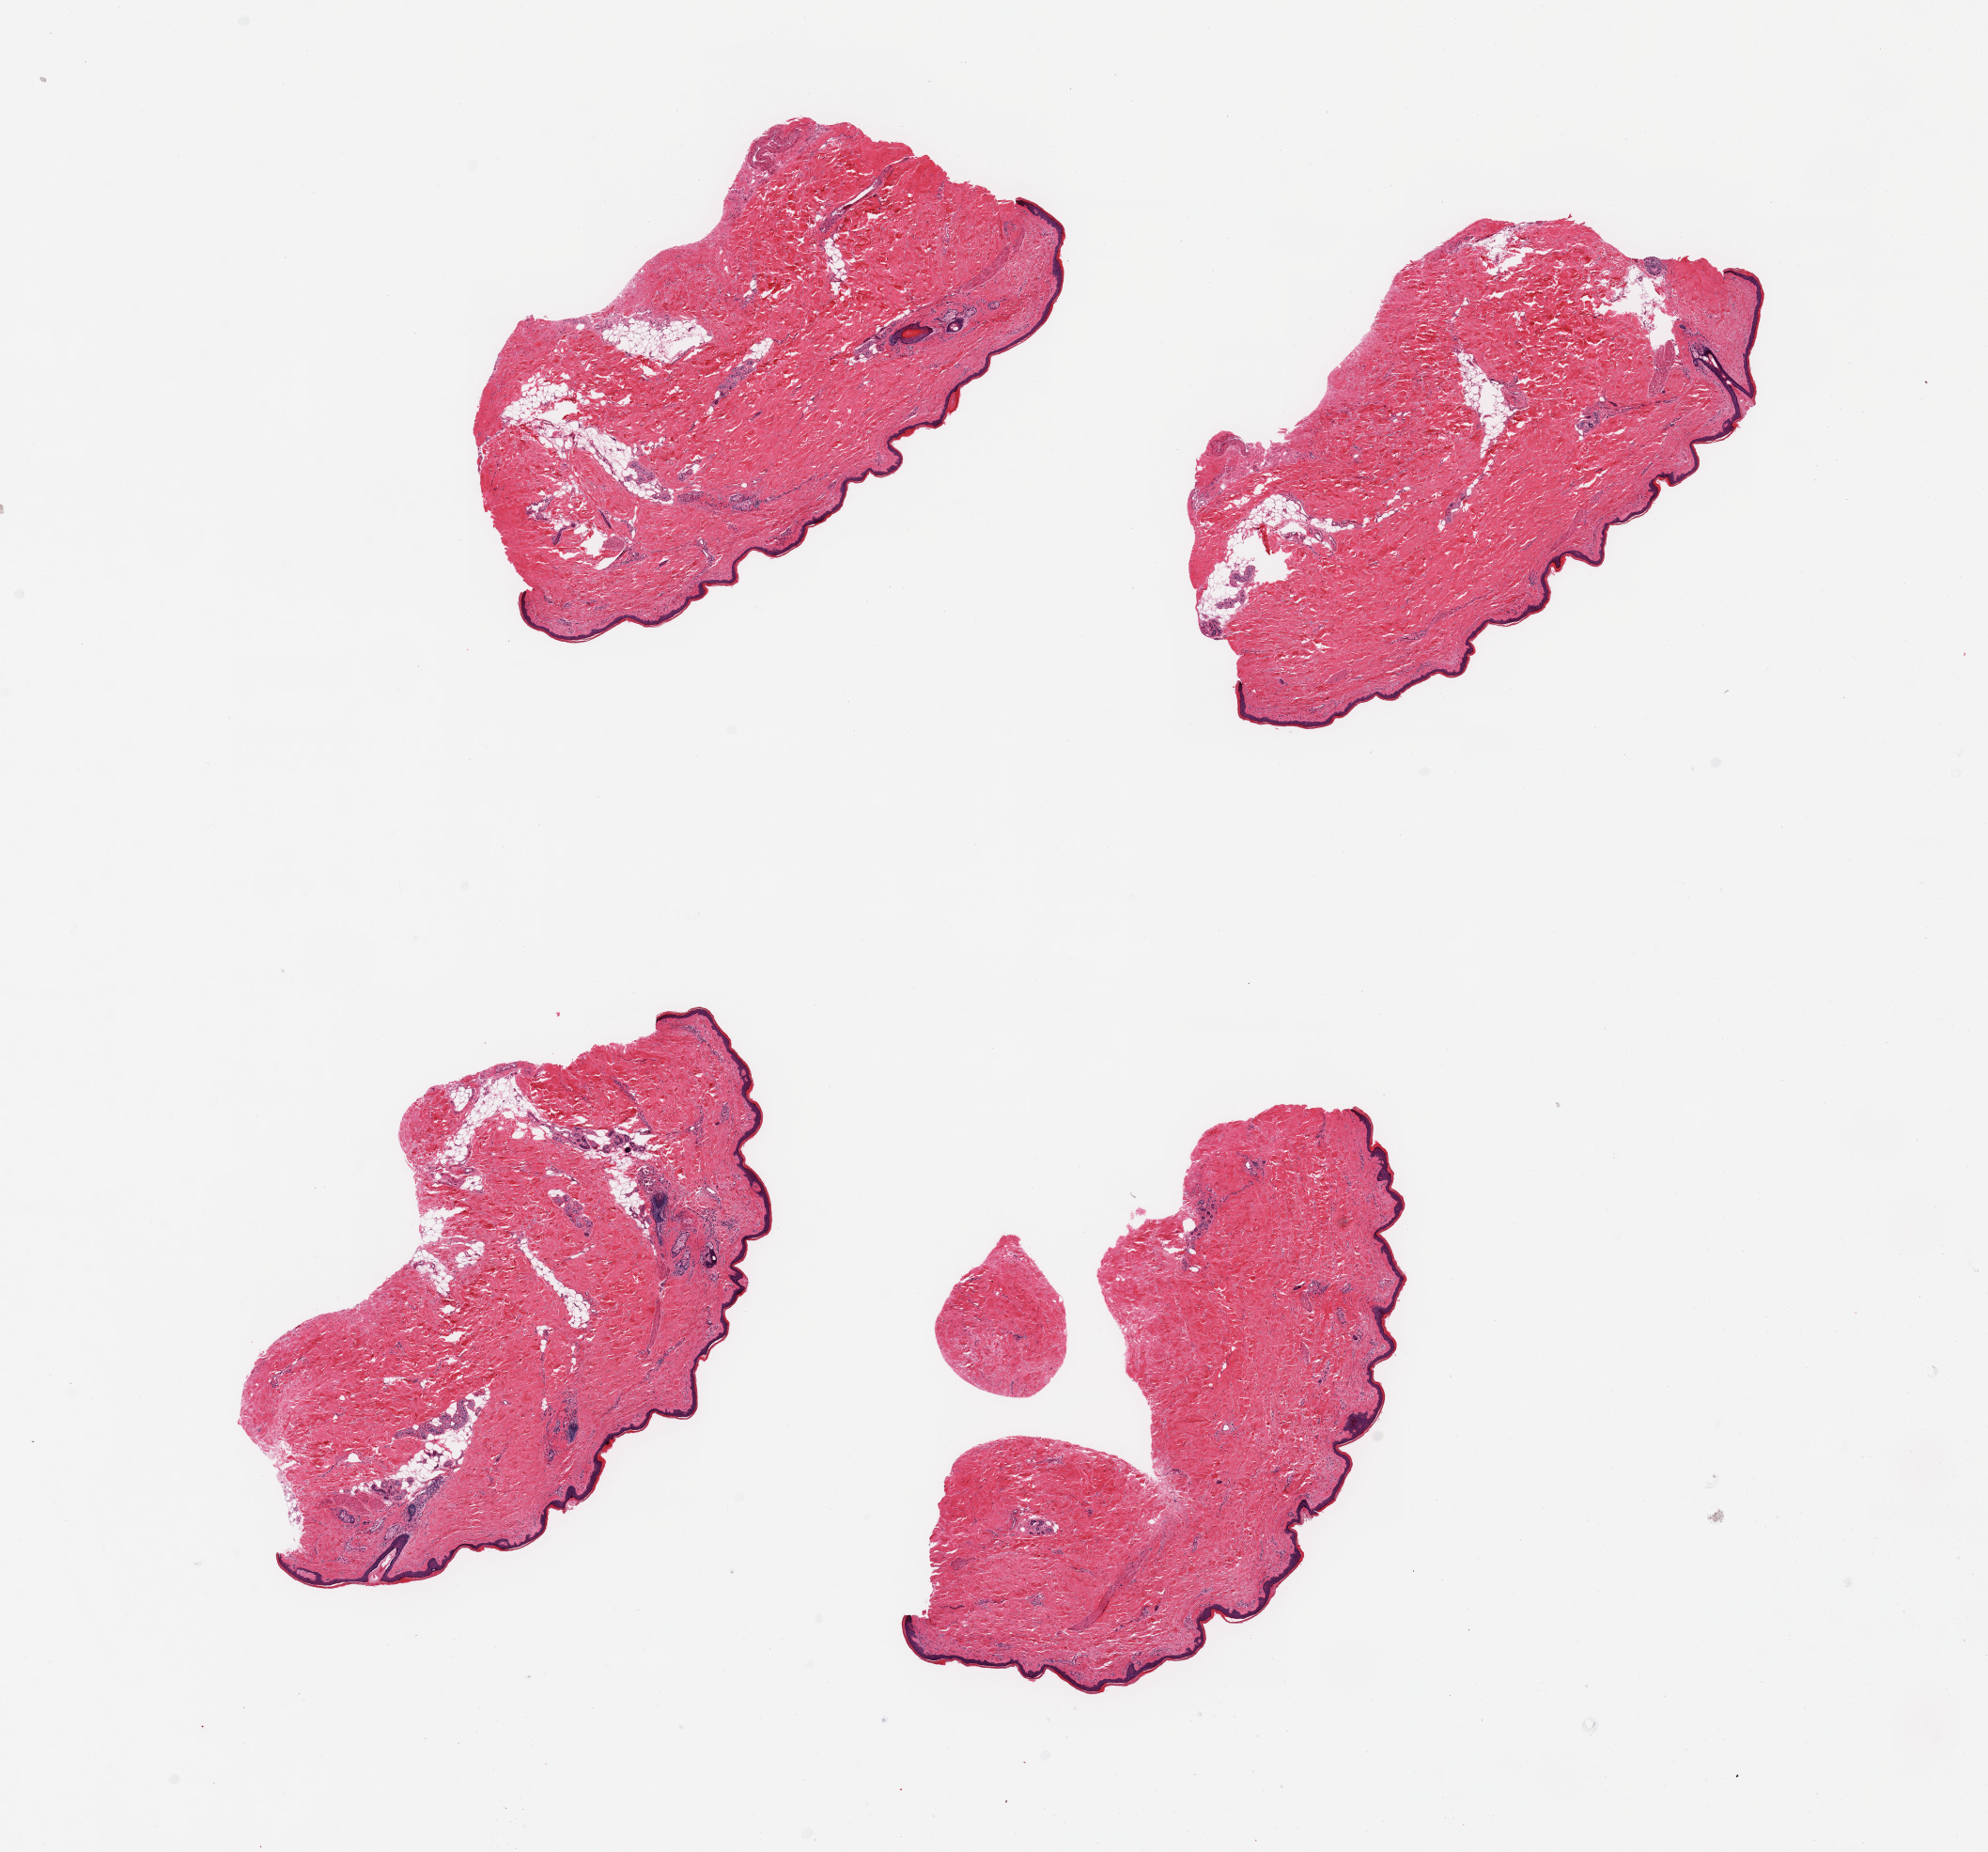
Whole-slide image, haematoxylin and eosin stain — a low-resolution overview of the entire scanned area, about 16.7 x 15.6 mm (slide scanned at 20x). PAXgene-fixed, paraffin-embedded tissue. Sampled site (target tissue): skin of lower leg. Donor tissue sample. Female donor.
Pathologist's review note for this sample: 4 pieces; well trimmed; 10% dermal fat.